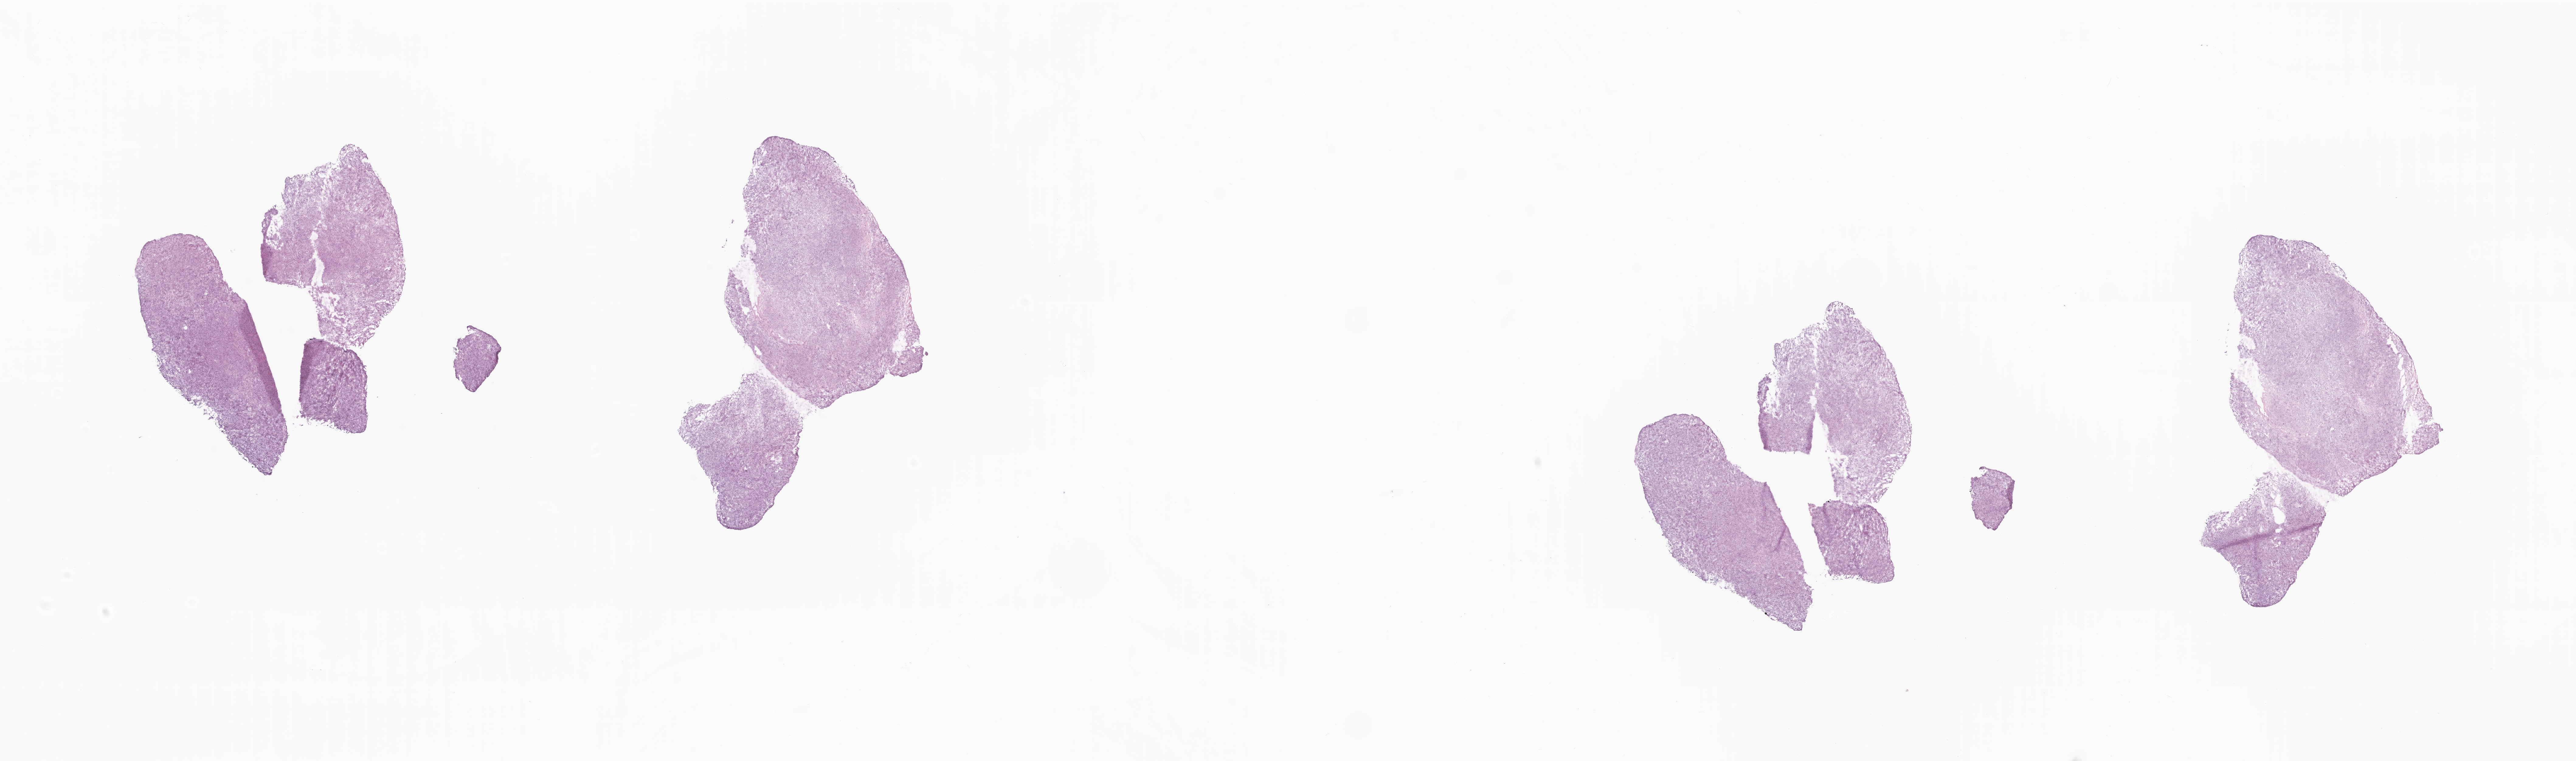
Digitized H&E-stained section — a low-resolution overview of the entire scanned area, about 35.7 x 10.5 mm; frozen section (tissue freezing medium); primary tumor; anatomic site: pancreas. Patient: female, age at initial diagnosis 76 years. Slide review estimates, as recorded: tumor cells 90%, tumor nuclei 95%.
Histologic diagnosis: Leiomyosarcoma, NOS.